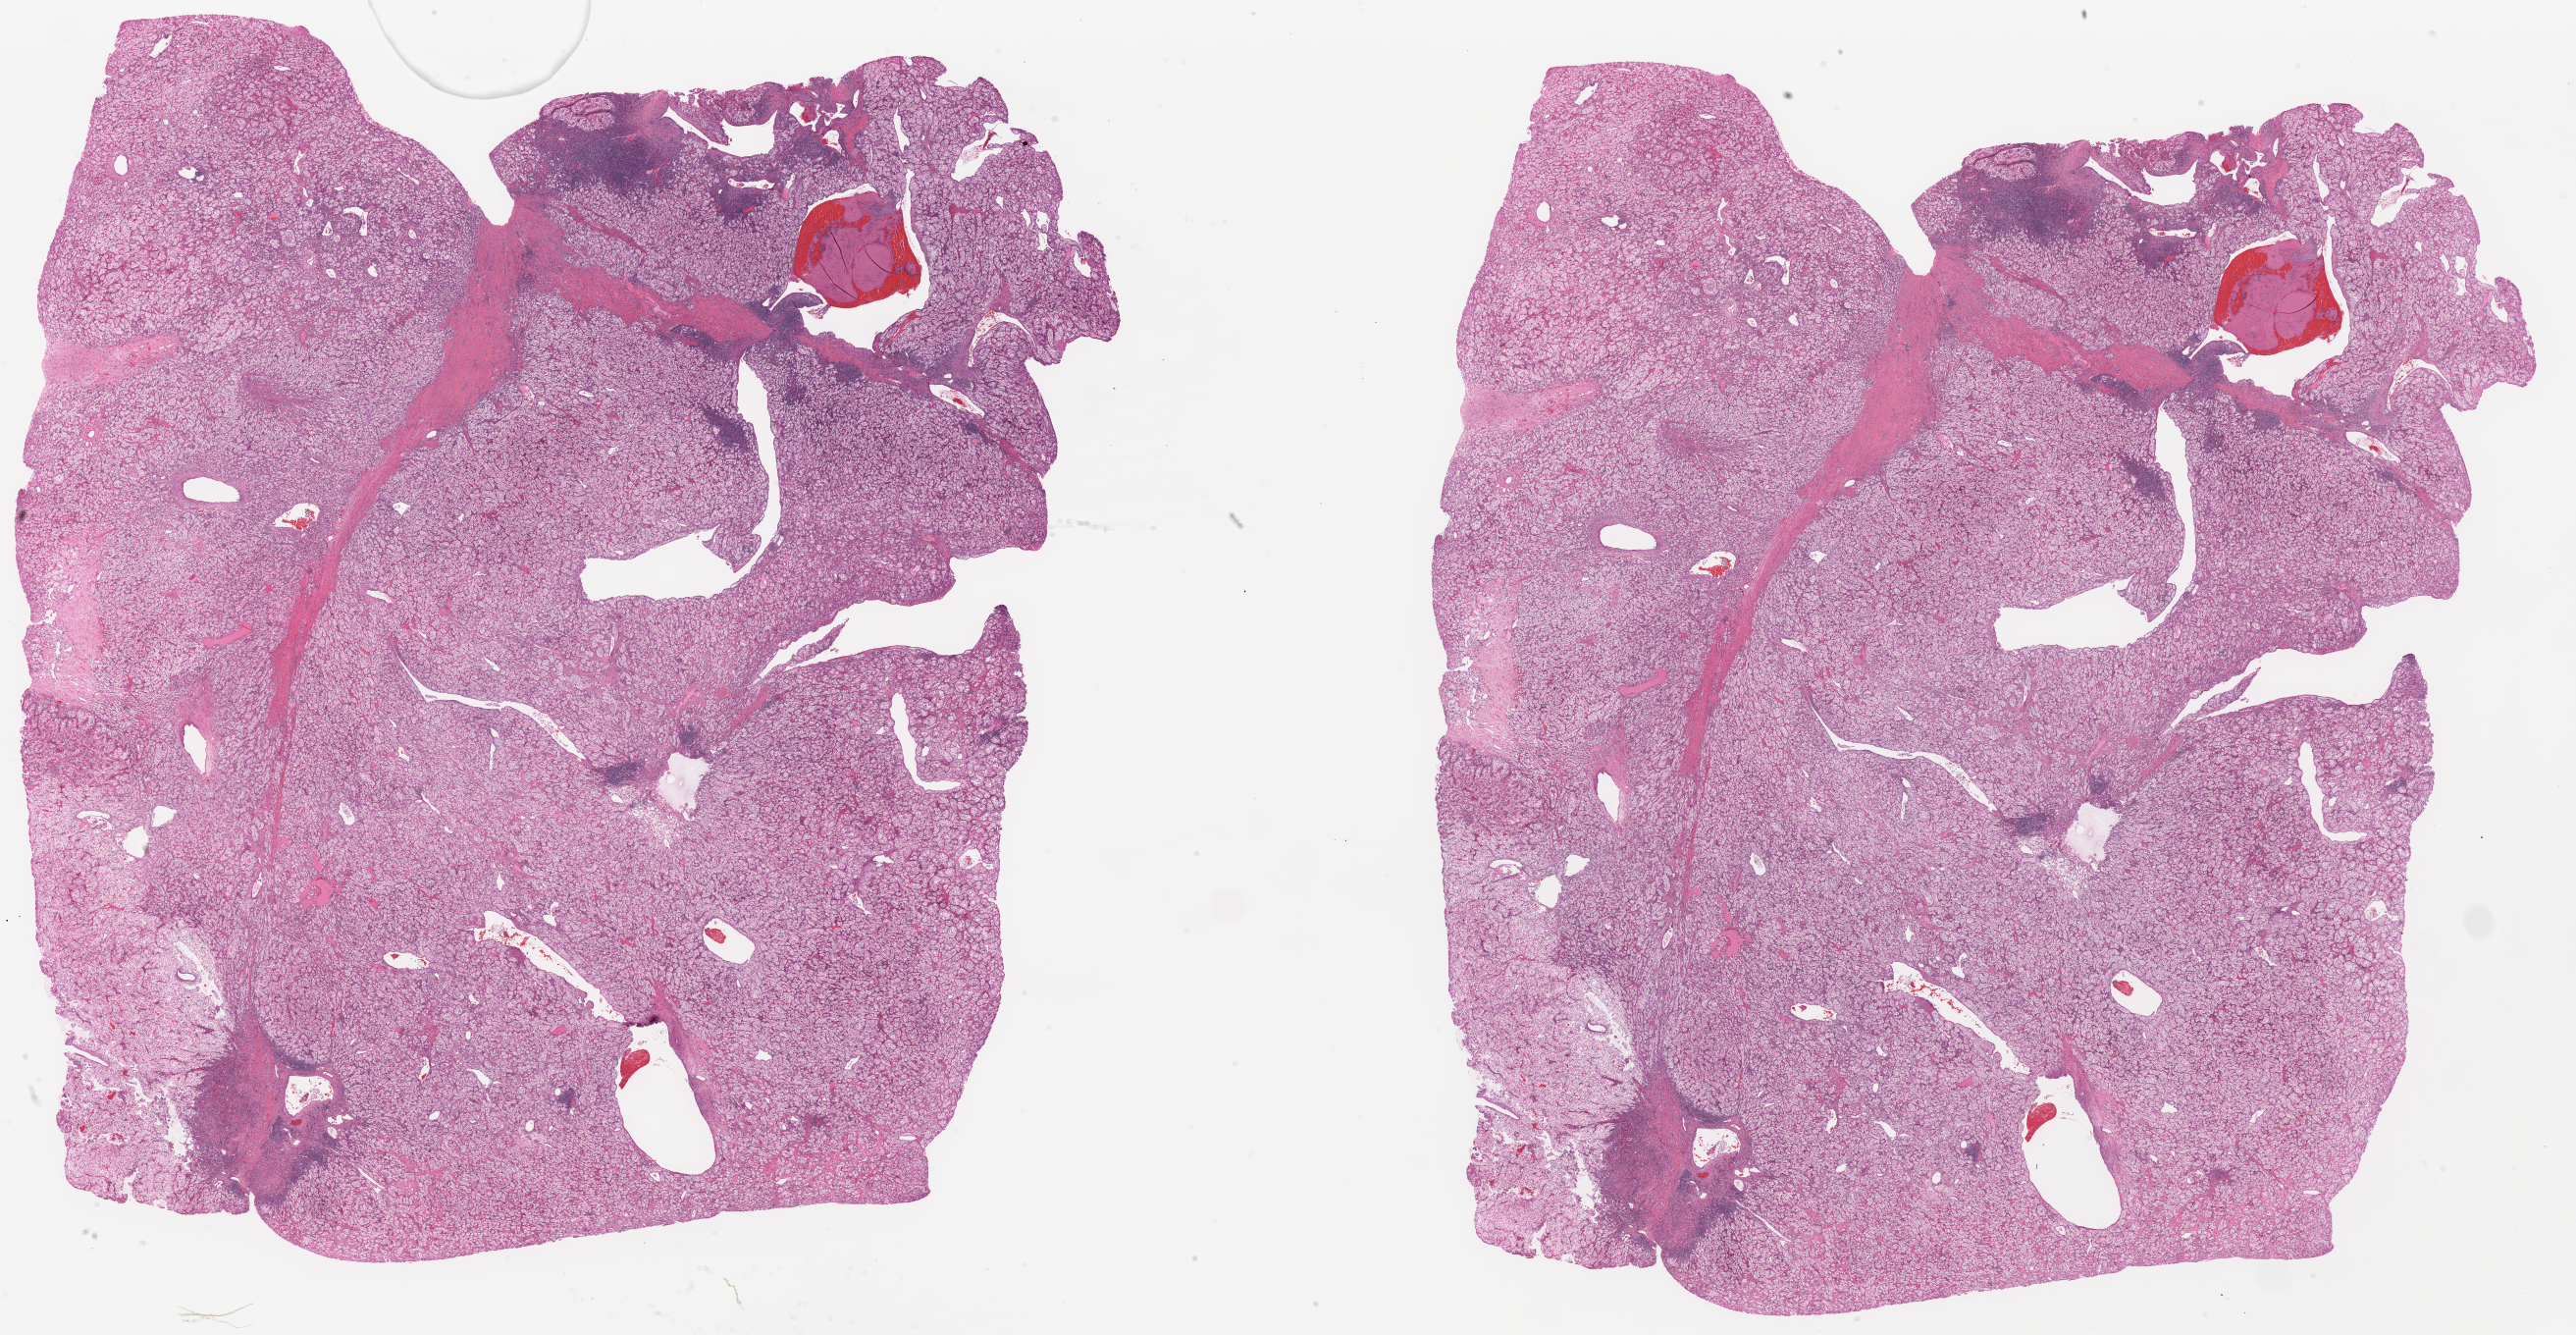
Hematoxylin and eosin (H&E) stained whole-slide image — low-resolution overview of the scanned area, about 41.5 x 21.5 mm (acquisition: 20x scan), formalin-fixed paraffin-embedded (FFPE) diagnostic section, kidney, primary tumour sample. Patient: male, age at initial diagnosis 56 years. Histologic grade: G4 (undifferentiated).
• lymph nodes positive (case pathology): 1 of 15 examined
• histologic diagnosis: Clear cell adenocarcinoma, NOS
• AJCC pathologic stage: III (7th edition)
• laterality: left